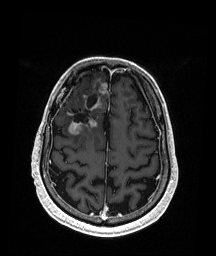
Brain MRI from a brain-tumour surgery series, one axial slice; position 54 of 192 along the scan axis; T1-weighted post-contrast; 216 × 256 image matrix, field of view 211 × 250 mm. From the clinical record (not read from this slice): histopathology: Astrocytoma; WHO grade: 3; IDH mutation: yes.
Outlined on this slice (outlined manually by an expert reader):
- previous resection cavity: bounding box <66,93,98,124> (left, top, right, bottom; pixels)
- tumour: <68,84,108,136>